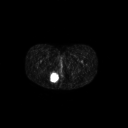
FDG PET of an extremity soft-tissue mass (from a PET/CT study), one axial slice; position 27 of 267 along the scan axis; 3.27 mm slice thickness; 128 × 128 image matrix, field of view 700 × 700 mm. Female patient, age 17 years. From the clinical record (not read from this slice): histological type: epithelioid sarcoma; grade: intermediate; site of the primary tumour: right buttock.
Annotated regions visible in this slice (expert contour drawn on MRI and transferred to this co-registered scan by the dataset authors):
- gross tumour volume including surrounding oedema: bounding box <49,71,59,83> (left, top, right, bottom; pixels)
- gross tumour volume (mass): <49,72,59,82>